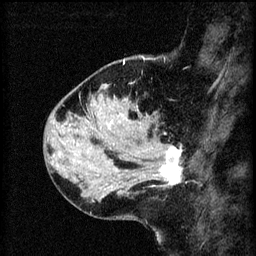
Breast MRI (dynamic contrast-enhanced), one sagittal slice; position 21 of 60 along the scan axis; 3 images stored at this slice position (order not interpretable as contrast timing); 1.5 T; TE 4.2 ms, TR 8.2 ms; 256 × 256 image matrix, field of view 180 × 180 mm. Patient: female, 37 years.
Annotated regions visible in this slice (semi-automatically segmented with operator editing):
- analysis volume of interest (the breast-tissue region the enhancement analysis was run in; not a lesion): bounding box (x1, y1, x2, y2) in pixels: (124, 138, 183, 195)
- tumour enhancement mask (voxels above the 70 % enhancement threshold inside the analysis volume of interest): (155, 146, 182, 185)